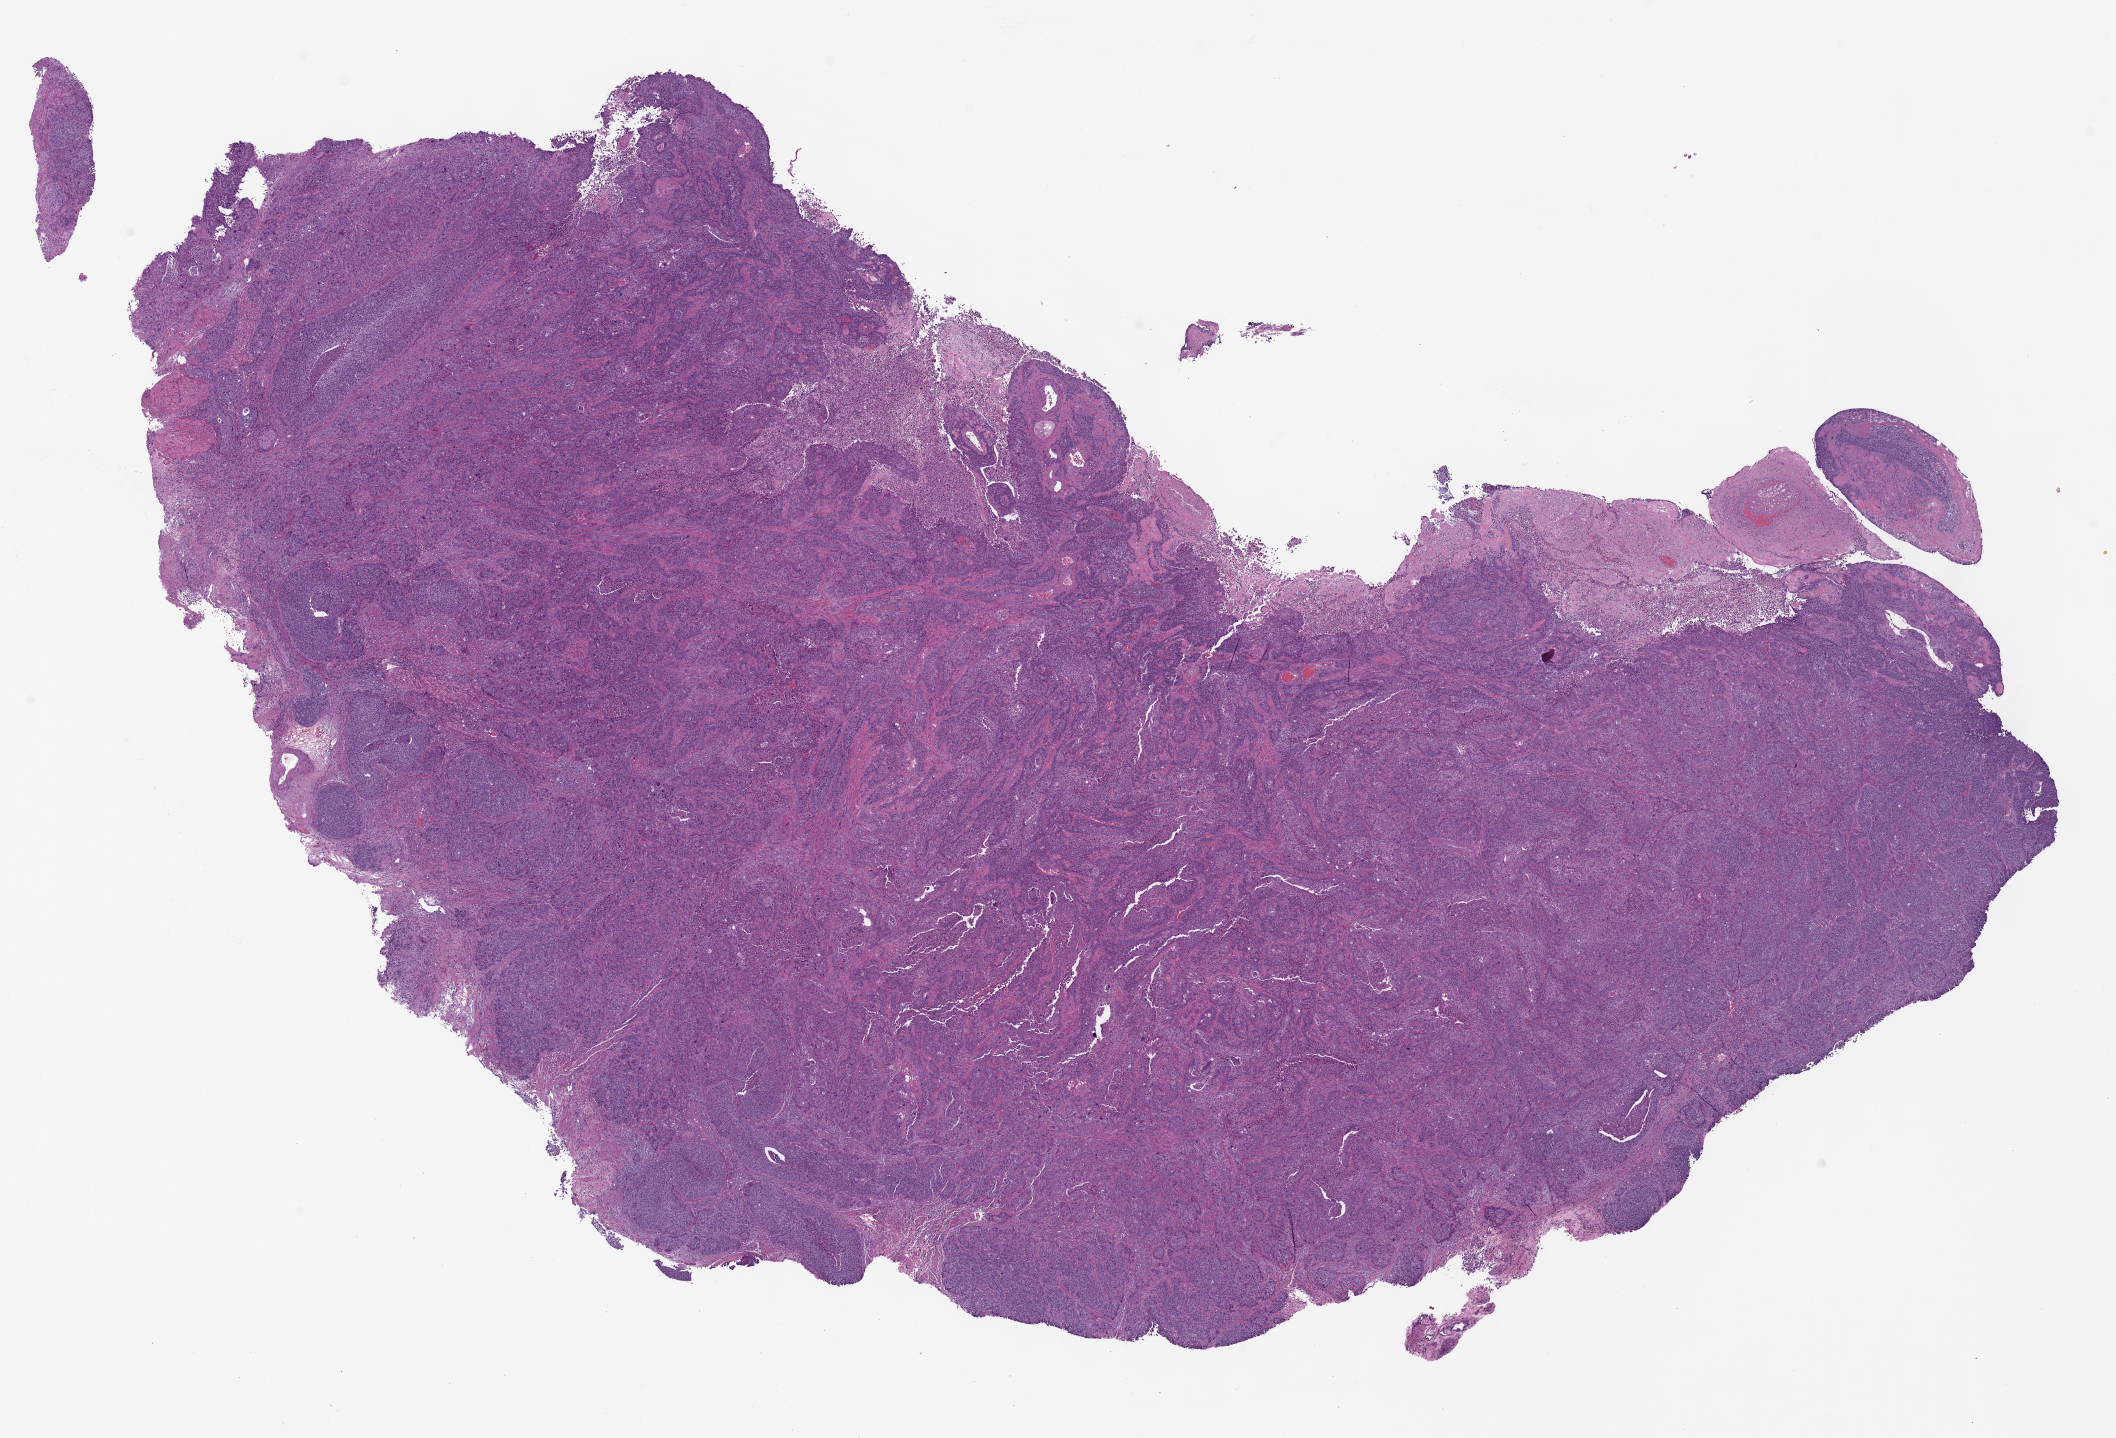
H&E-stained whole-slide image — whole scanned area (about 16.6 x 11.3 mm, from a 40x scan) shown as a low-resolution overview, formalin-fixed paraffin-embedded (FFPE) diagnostic section, cervix, primary tumour sample. Patient: female, age at initial diagnosis 47 years. Histologic grade: G2 (moderately differentiated).
- pathologic diagnosis: Squamous cell carcinoma, large cell, nonkeratinizing, NOS
- FIGO stage: IB2